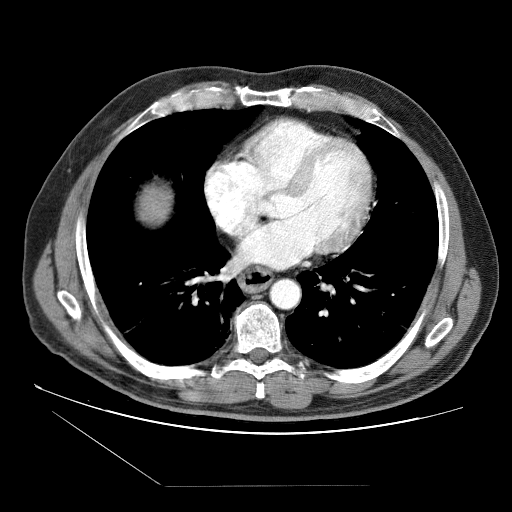
Contrast-enhanced abdominal CT (liver protocol), one axial slice. Slice 85 of 87 in the series (ordered by position). Reconstruction kernel STANDARD. 120 kVp. Soft-tissue window (W 400 / L 40 HU). 2.5 mm slice thickness. 512 × 512 image matrix, field of view 400 × 400 mm. From the clinical record (not read from this slice): diagnosis: hepatocellular carcinoma (patient treated with transarterial chemoembolisation; whether this scan precedes or follows treatment is not stated here); TNM stage (as recorded): Stage-II; Child-Pugh class: B; tumour size: 2.6 cm.
Structures marked on this image (semi-automatic segmentation, software-assisted and operator-edited):
- liver parenchyma outside the tumour (the mass and vessels are separate outlines, so this box may not span the whole liver): bounding box <138,185,172,222> (left, top, right, bottom; pixels)